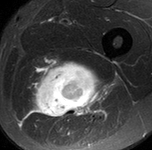
MRI of an extremity soft-tissue mass, one axial slice. Slice 79 of 90 in the series (ordered by position). STIR. MR volume resampled by the dataset authors to the PET/CT grid (not the native acquisition matrix). 152 × 150 image matrix, field of view 148 × 146 mm. Male patient. From the clinical record (not read from this slice): histological type: undifferentiated pleomorphic liposarcoma; grade: high; site of the primary tumour: left thigh.
Outlined on this slice (expert contour drawn on MRI and transferred to this co-registered scan by the dataset authors):
- gross tumour volume including surrounding oedema: bounding box (x1, y1, x2, y2) in pixels: (25, 59, 112, 122)
- gross tumour volume (mass): (32, 60, 104, 118)